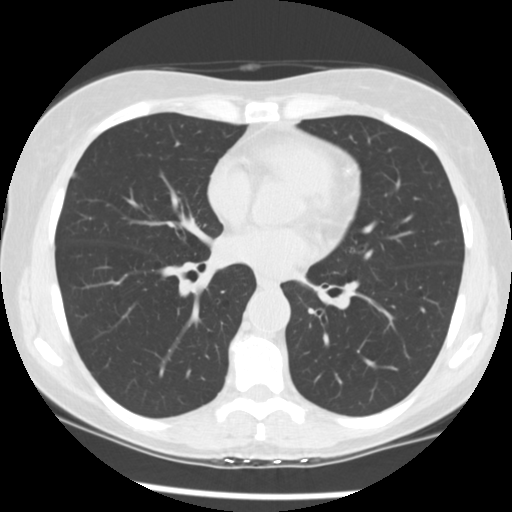
Low-dose screening chest CT, one axial slice; slice 128 of 241 in the series (ordered by position); reconstruction kernel STANDARD; lung window (W 1500 / L -600 HU); 2.5 mm slice thickness; 512 × 512 image matrix, field of view 320 × 320 mm.
Outlined on this slice (outlined manually by an expert reader):
- lesion 1 (tumor, upper lobe of right lung): bounding box [x1, y1, x2, y2] px = [72, 172, 77, 179]